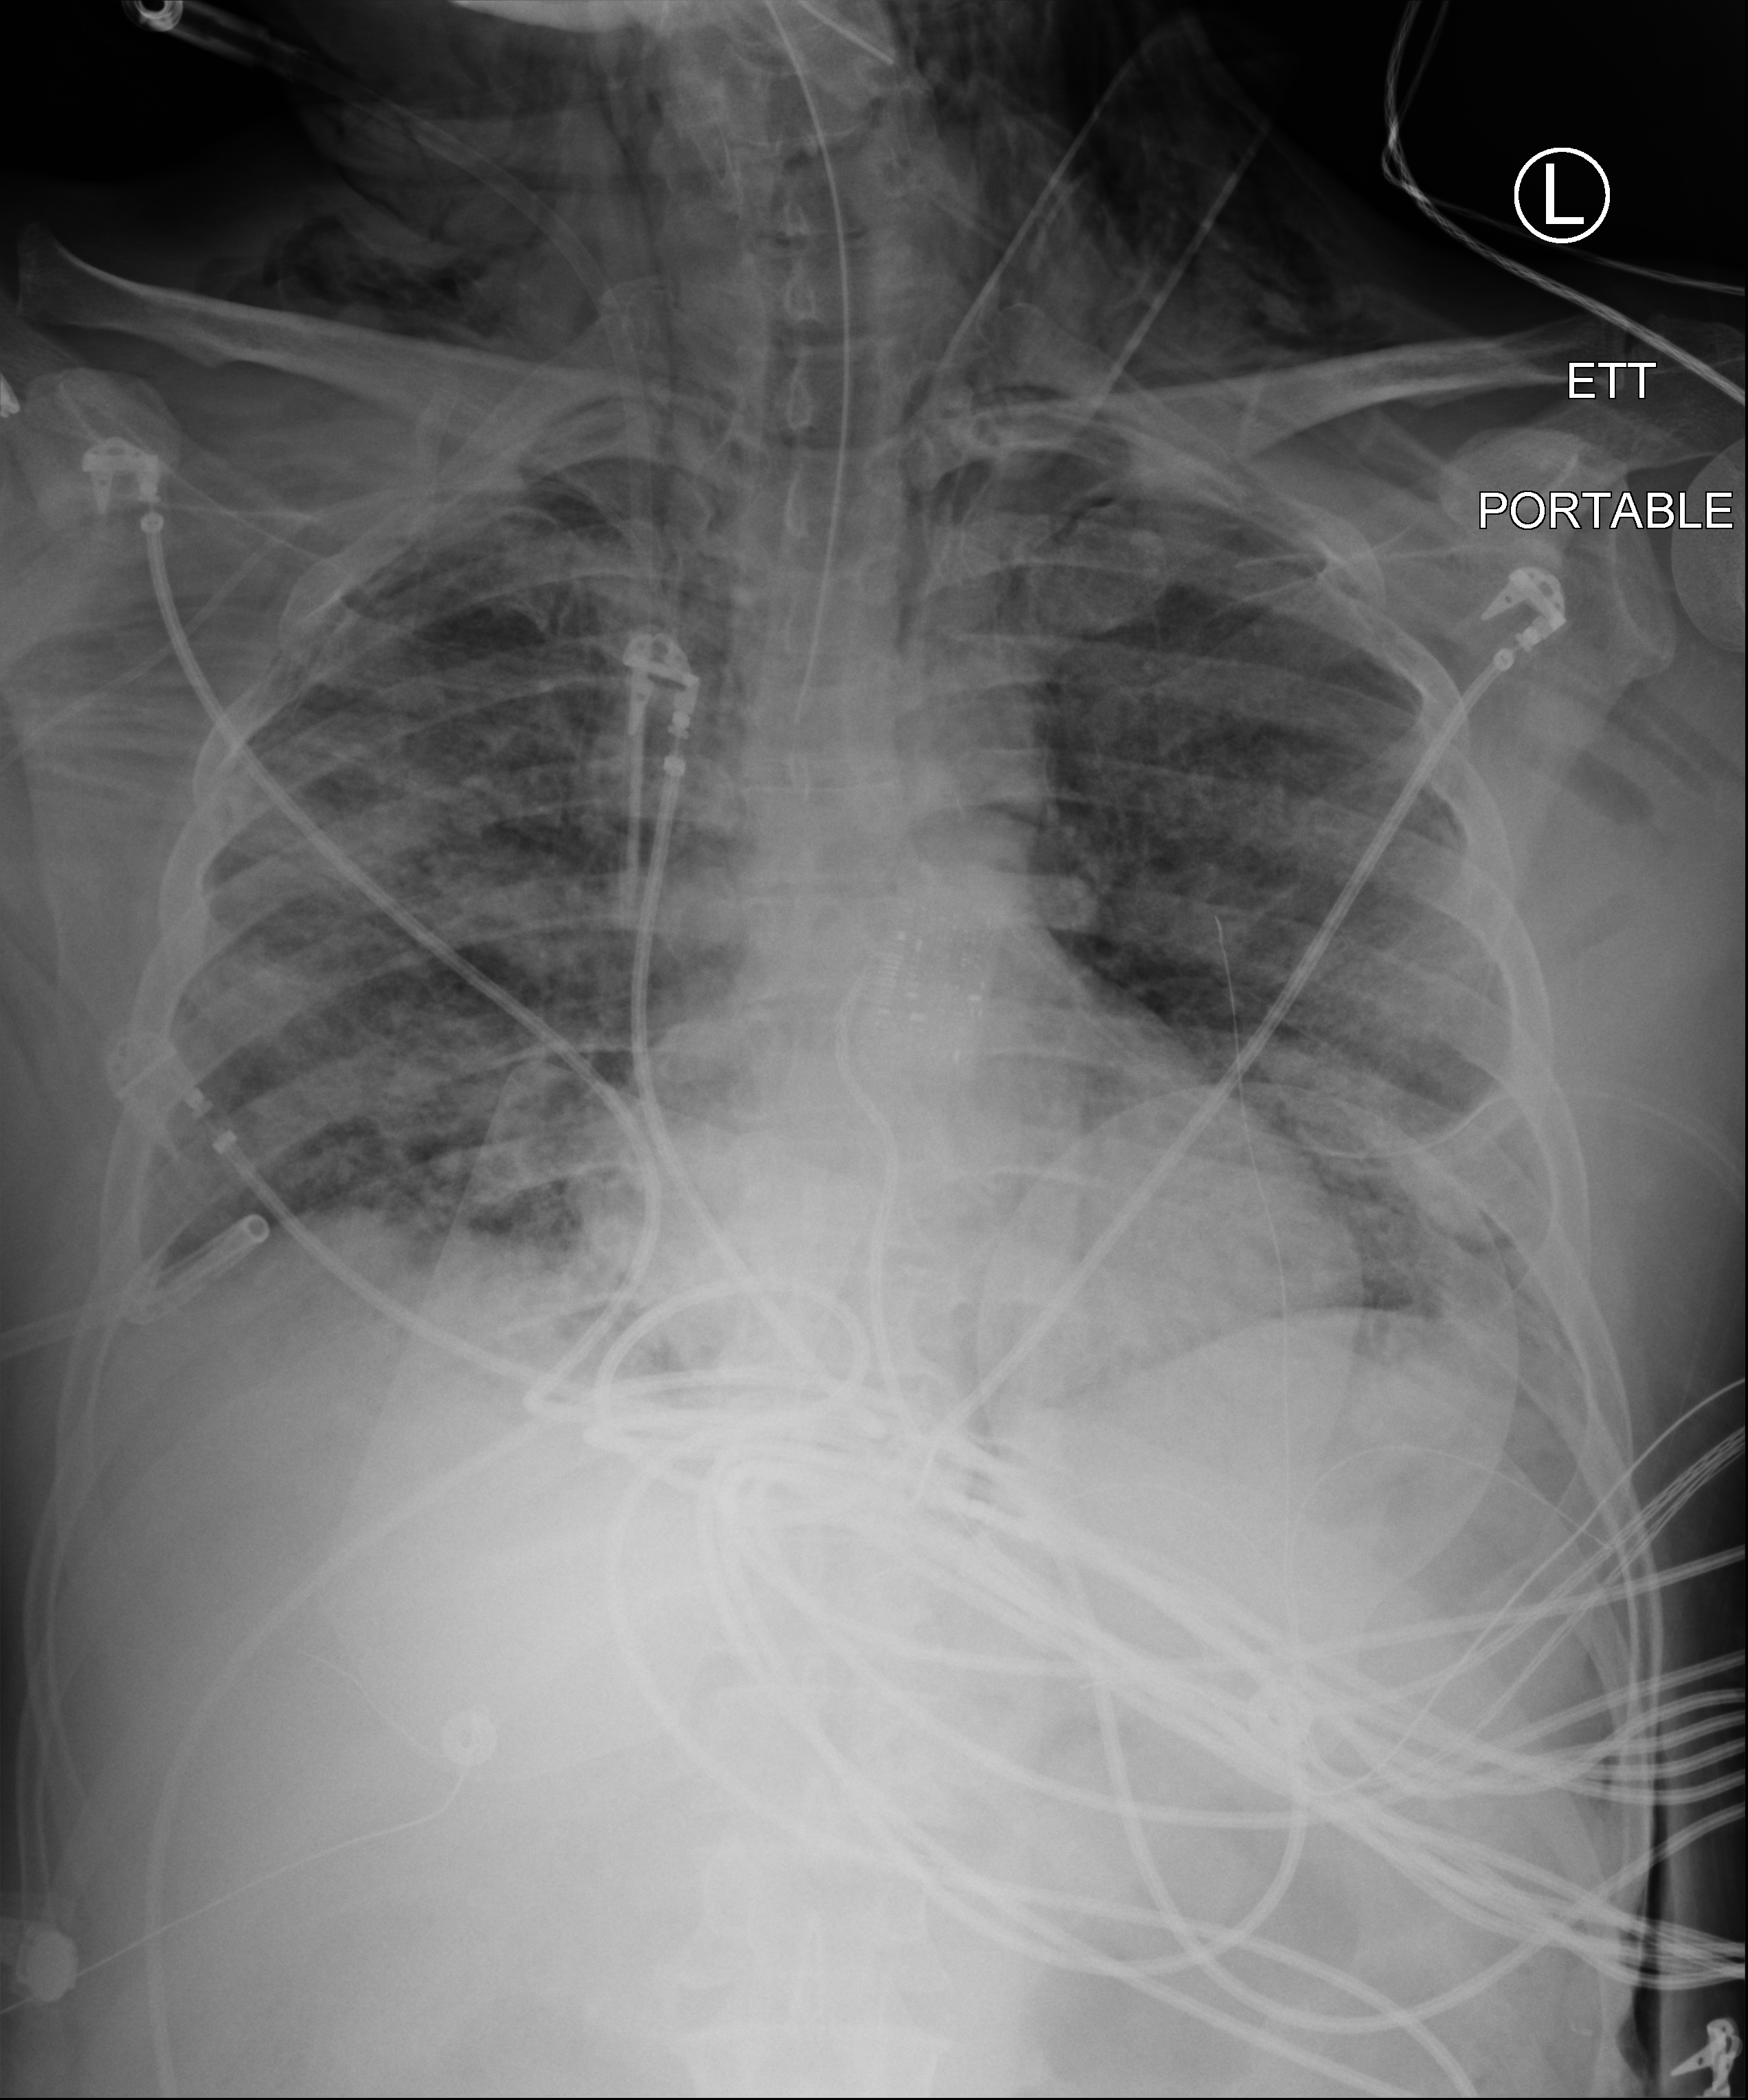
Bedside chest radiograph (computed radiography). Male patient hospitalised with COVID-19, age 18–59 years.
Hospital-stay facts (about this admission, not read from this image; timing relative to this image not recorded):
- length of hospital stay: 77 days
- admitted to intensive care during this hospital stay: yes